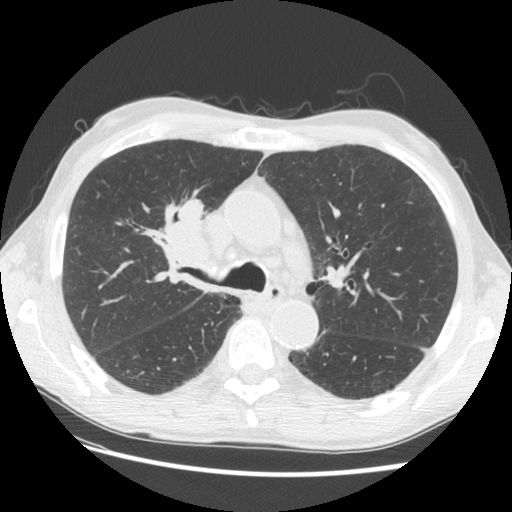
Low-dose screening chest CT, axial slice, third screening round (two years after baseline), lung window (W 1500 / L -600 HU), 2.5 mm slice thickness, slice 45 of 133 in the series, 512 × 512 image matrix. Male participant, aged 73 years at enrolment. Current smoker at enrolment.
- Expert reader's lesion annotation, box from (x=141, y=186) to (x=234, y=275) px.
- The screening reader recorded 4 non-calcified nodules or masses ≥4 mm on this exam (right upper lobe, right upper lobe, right upper lobe, left lower lobe); which of them this box marks is not recorded.
- Lung cancer was diagnosed 48 days after this screen: squamous cell carcinoma, NOS, right upper lobe, poorly differentiated (G3), stage IIIB (AJCC 6th edition), 56 mm at pathology.